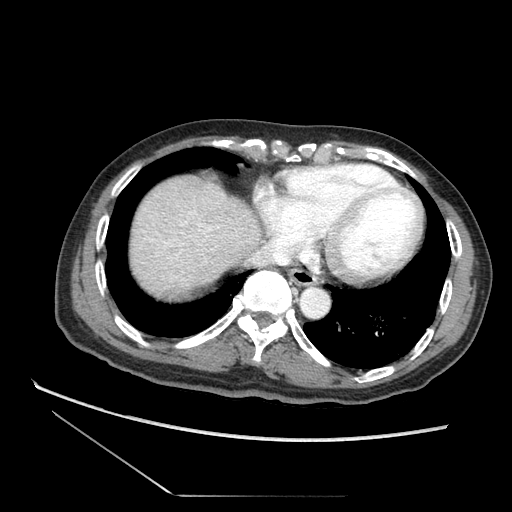
Contrast-enhanced abdominal CT (liver protocol), one axial slice; position 69 of 73 along the scan axis; reconstruction kernel STANDARD; soft-tissue window (W 400 / L 40 HU); 2.5 mm slice thickness; 512 × 512 image matrix. Case-level facts recorded for this patient, not image findings: diagnosis: hepatocellular carcinoma (patient treated with transarterial chemoembolisation; whether this scan precedes or follows treatment is not stated here); TNM stage (as recorded): Stage-II; Child-Pugh class: A; tumour nodularity: multinodular; tumour size: 3.8 cm.
Annotated regions visible in this slice (semi-automatic segmentation, software-assisted and operator-edited):
- abdominal aorta: bounding box (x1, y1, x2, y2) in pixels: (302, 287, 330, 317)
- liver parenchyma outside the tumour (the mass and vessels are separate outlines, so this box may not span the whole liver): (122, 172, 270, 304)
- liver vessels: (196, 248, 207, 266)